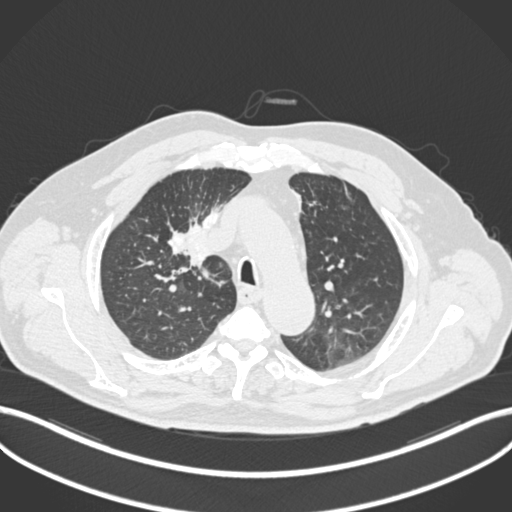
Chest CT, one axial slice. Position 149 of 255 along the scan axis. 120 kVp. Lung window (W 1500 / L -600 HU). 1 mm slice thickness. 512 × 512 image matrix, field of view 400 × 400 mm. Male patient, age 60 years. Case-level facts recorded for this patient, not image findings: clinical TNM (as recorded): T1b N1 M0.
Structures marked on this image (rectangle marked by the reading radiologist):
- lung tumour (recorded histology: squamous cell carcinoma): bounding box [x1, y1, x2, y2] px = [166, 224, 211, 283]